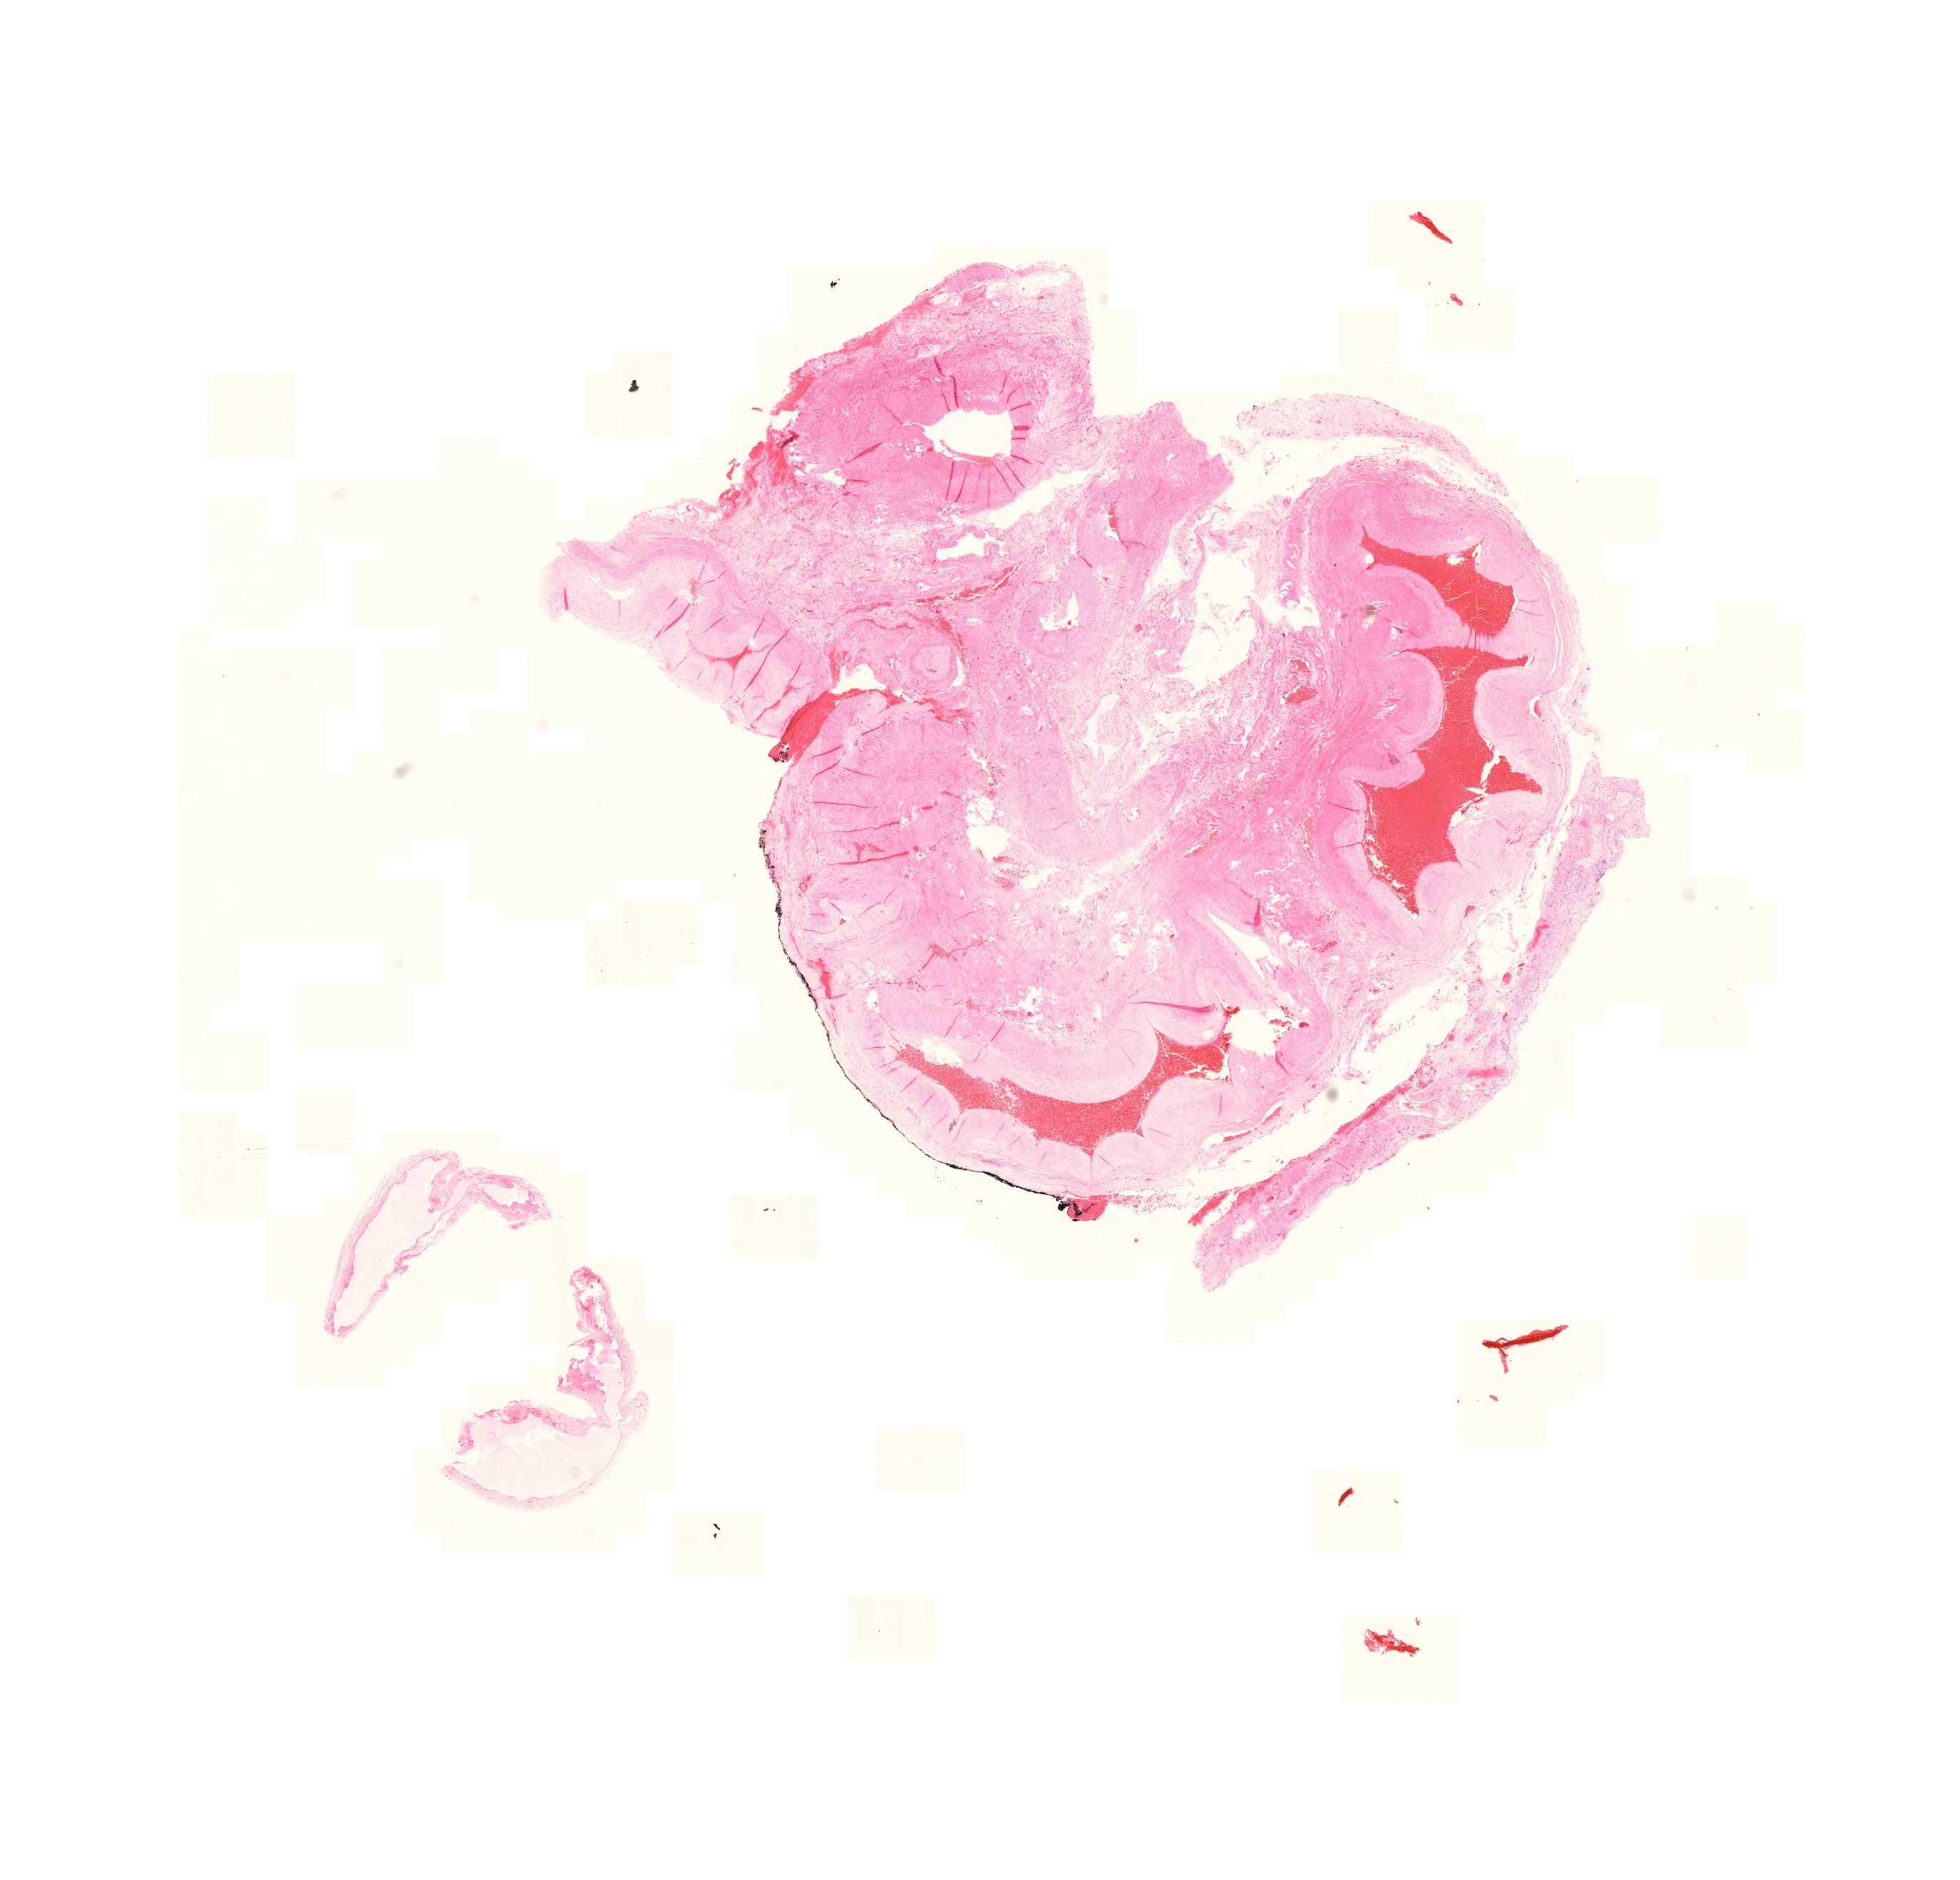
Digitized H&E tissue section (whole slide), a low-resolution overview of the entire scanned area, about 20.4 x 19.6 mm. FFPE section. Colon, primary tumour sample. Patient: male, age at initial diagnosis 82 years.
- AJCC pathologic stage: IIA (7th edition)
- TNM: T3 N0 M0
- histologic diagnosis: Adenocarcinoma, NOS